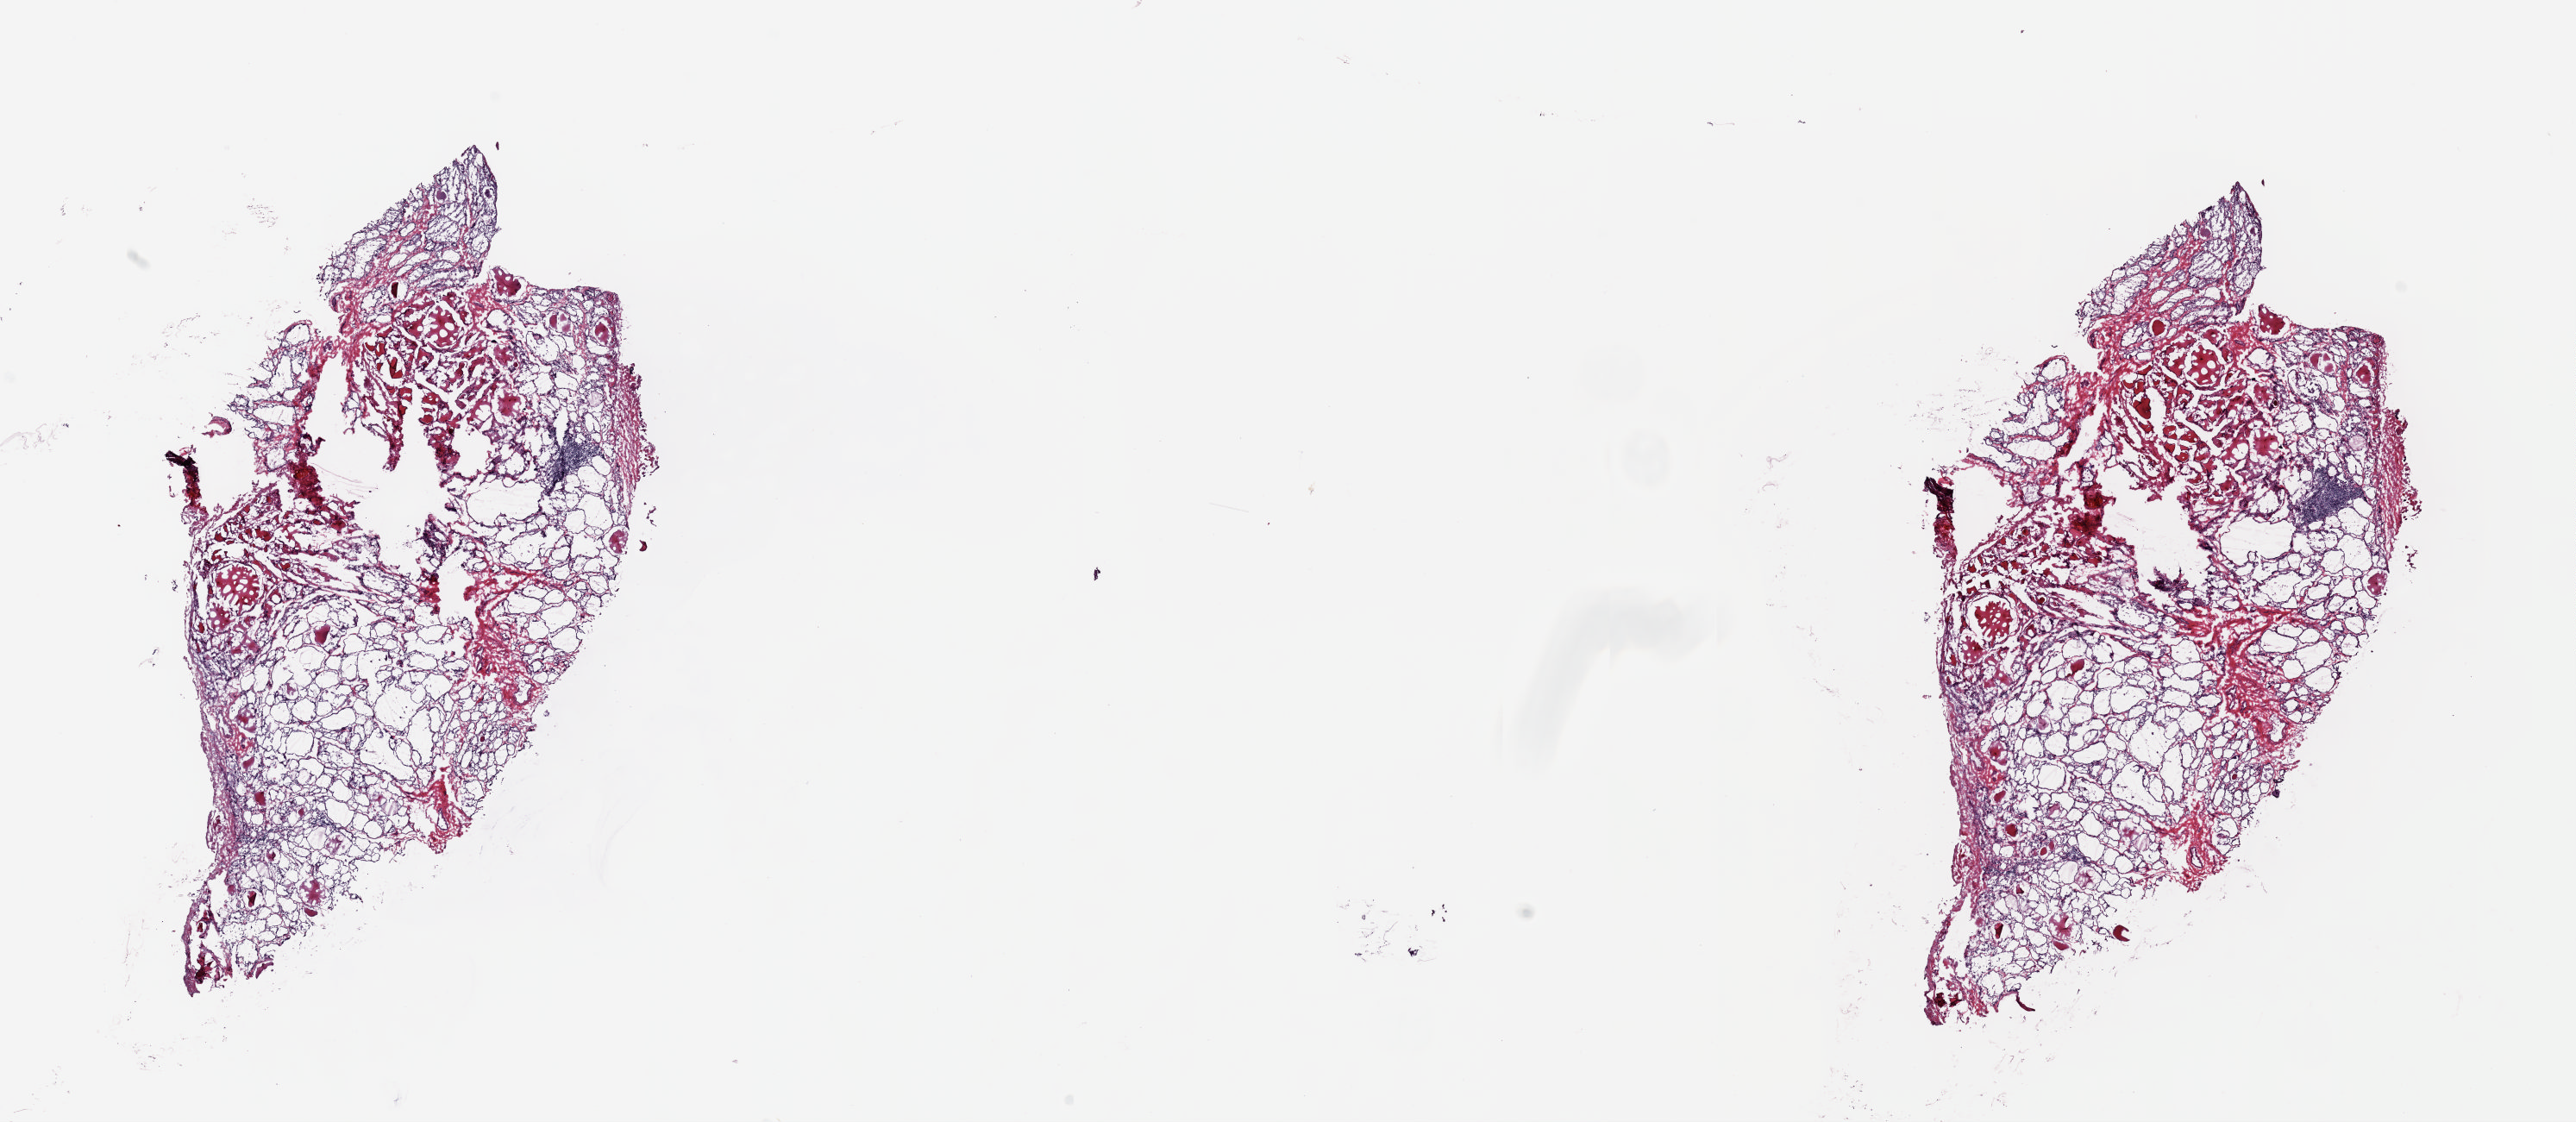
Whole-slide histology image, H&E, shown as a low-resolution overview of the whole scanned area (about 23.6 x 10.3 mm), frozen section, thyroid, solid tissue normal (non-tumour tissue) sample. Patient: female, age at initial diagnosis 78 years. Composition of this section per pathologist review: tumour cells 0%, tumour nuclei 0%, normal cells 100%, stromal cells 0%, necrosis 0%. Inflammatory infiltration, as recorded: lymphocyte infiltration 0%, monocyte infiltration 0%, neutrophil infiltration 0%.
* this section: solid tissue normal sample (biorepository sample class)
* patient diagnosis: Papillary adenocarcinoma, NOS